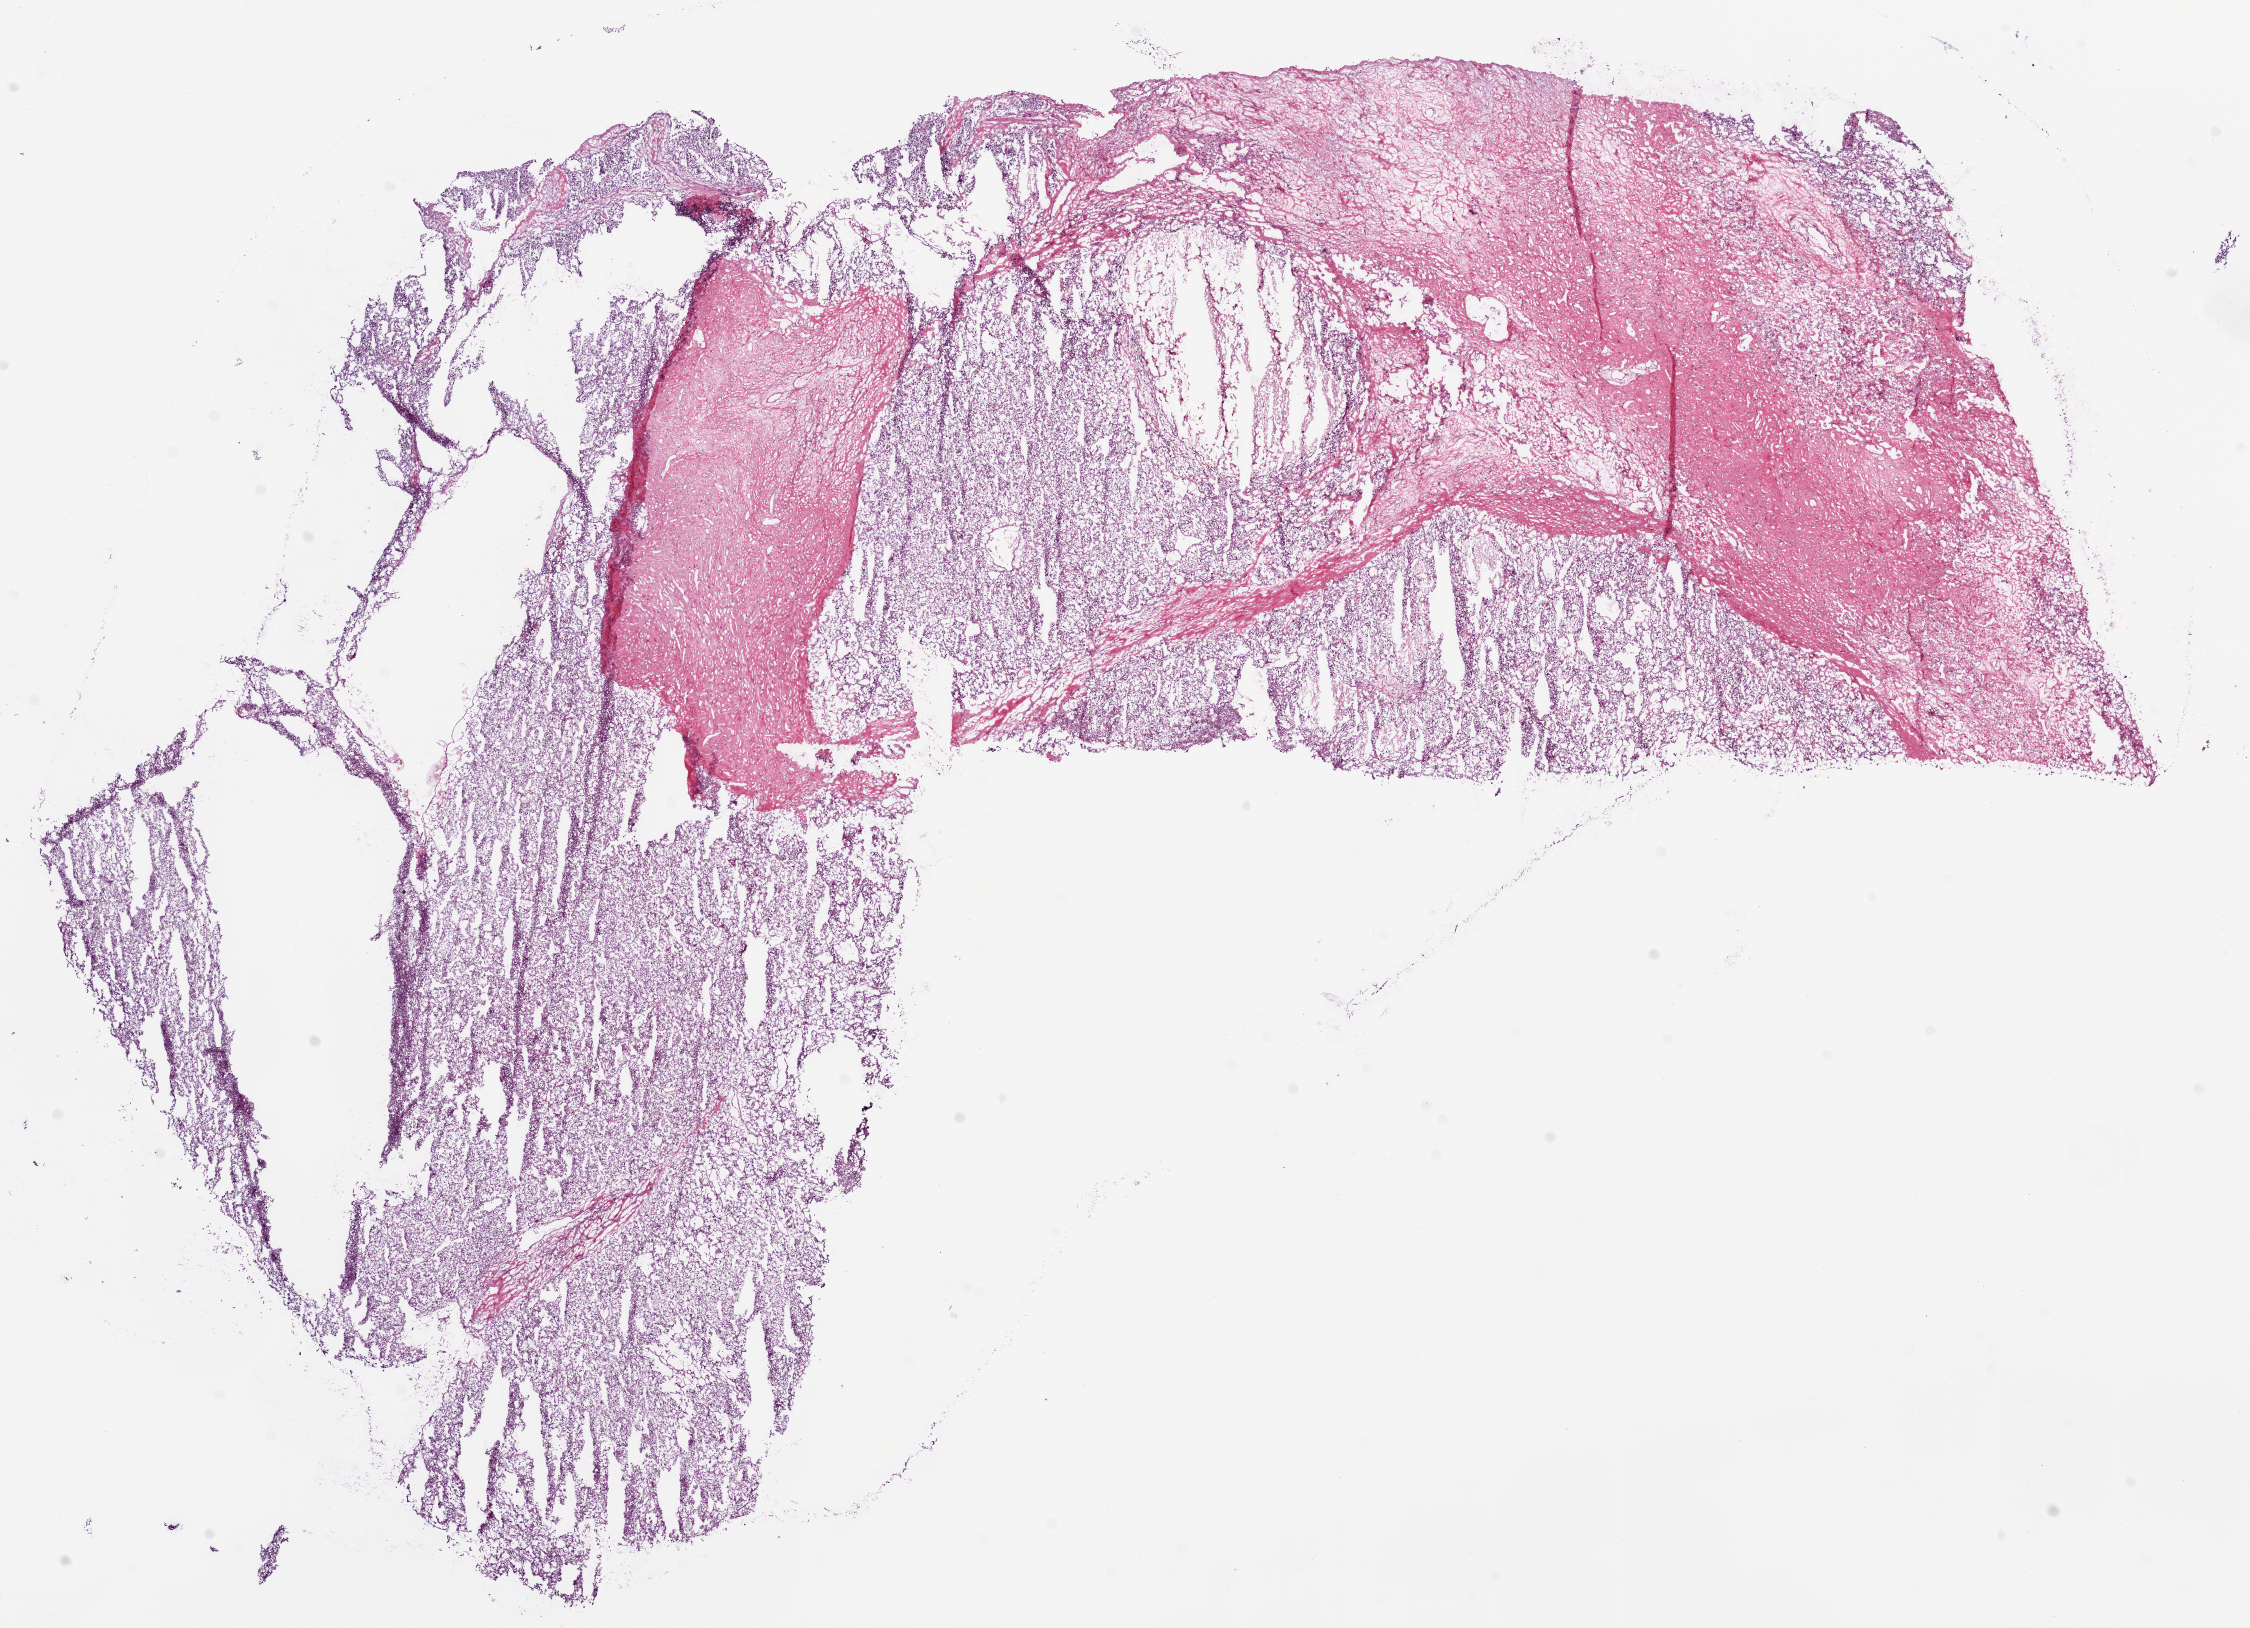
Digitized H&E-stained tissue section (whole slide) — a low-resolution overview of the entire scanned area, about 18.1 x 13.1 mm; frozen section from the bottom of the tissue portion; primary tumour sample from the kidney. Patient: male, age at initial diagnosis 63 years. Pathologist review of this section (percent, as recorded): tumour cells 60%, tumour nuclei 80%.
Histologic diagnosis: Clear cell adenocarcinoma, NOS.